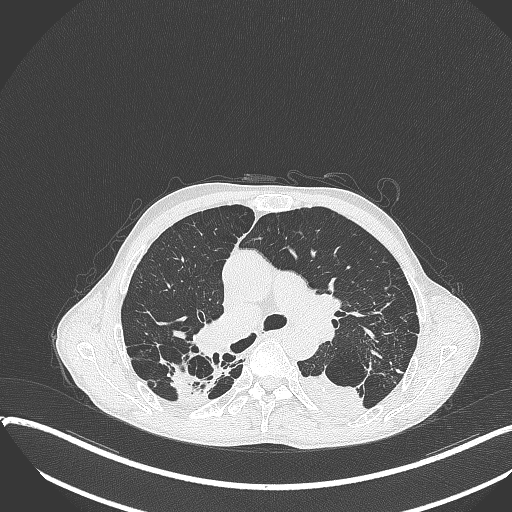
Chest CT, one axial slice. Slice 244 of 401 in the series (ordered by position). Reconstruction kernel B70f. 120 kVp. Lung window (W 1500 / L -600 HU). 1 mm slice thickness. 512 × 512 image matrix, field of view 400 × 400 mm. Male patient, age 57 years. Case-level facts recorded for this patient, not image findings: clinical TNM (as recorded): T4 N0 M0.
Outlined on this slice (rectangle marked by the reading radiologist):
- lung tumour (recorded histology: squamous cell carcinoma): box from (x=294, y=371) to (x=369, y=425) px